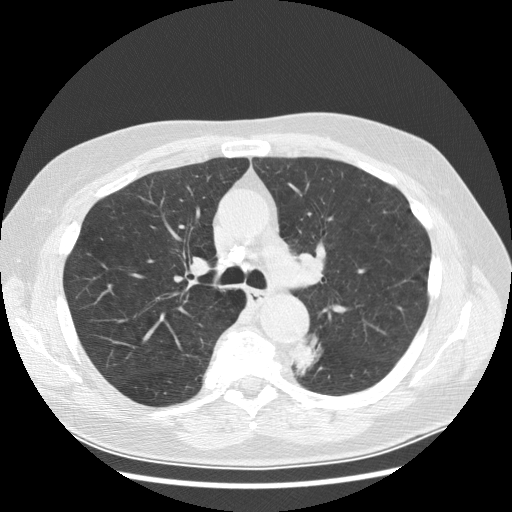
Low-dose screening chest CT, one axial slice. Slice 188 of 282 in the series (ordered by position). Reconstruction kernel STANDARD. Lung window (W 1500 / L -600 HU). 2.5 mm slice thickness. 512 × 512 image matrix.
Structures marked on this image (expert manual segmentation):
- lesion 1 (tumor, lower lobe of left lung): bounding box <293,337,321,376> (left, top, right, bottom; pixels)